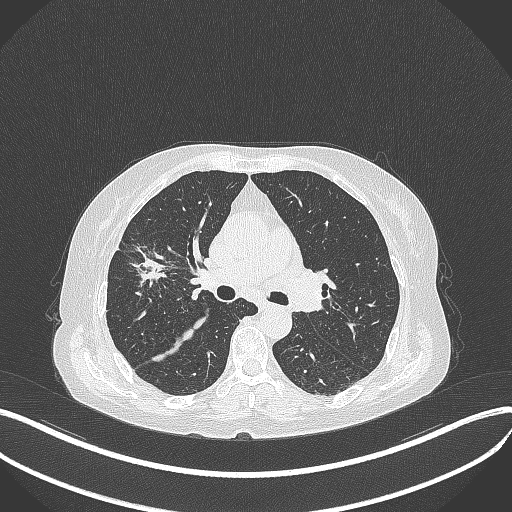
Chest CT, one axial slice. Slice 242 of 429 in the series (ordered by position). 120 kVp. Lung window (W 1500 / L -600 HU). 1 mm slice thickness. 512 × 512 image matrix. Female patient, age 69 years. Case-level facts recorded for this patient, not image findings: clinical TNM (as recorded): T1b N3 M0.
Annotated regions visible in this slice (rectangle marked by the reading radiologist):
- lung tumour (recorded histology: small cell carcinoma): bounding box (x1, y1, x2, y2) in pixels: (122, 244, 176, 293)